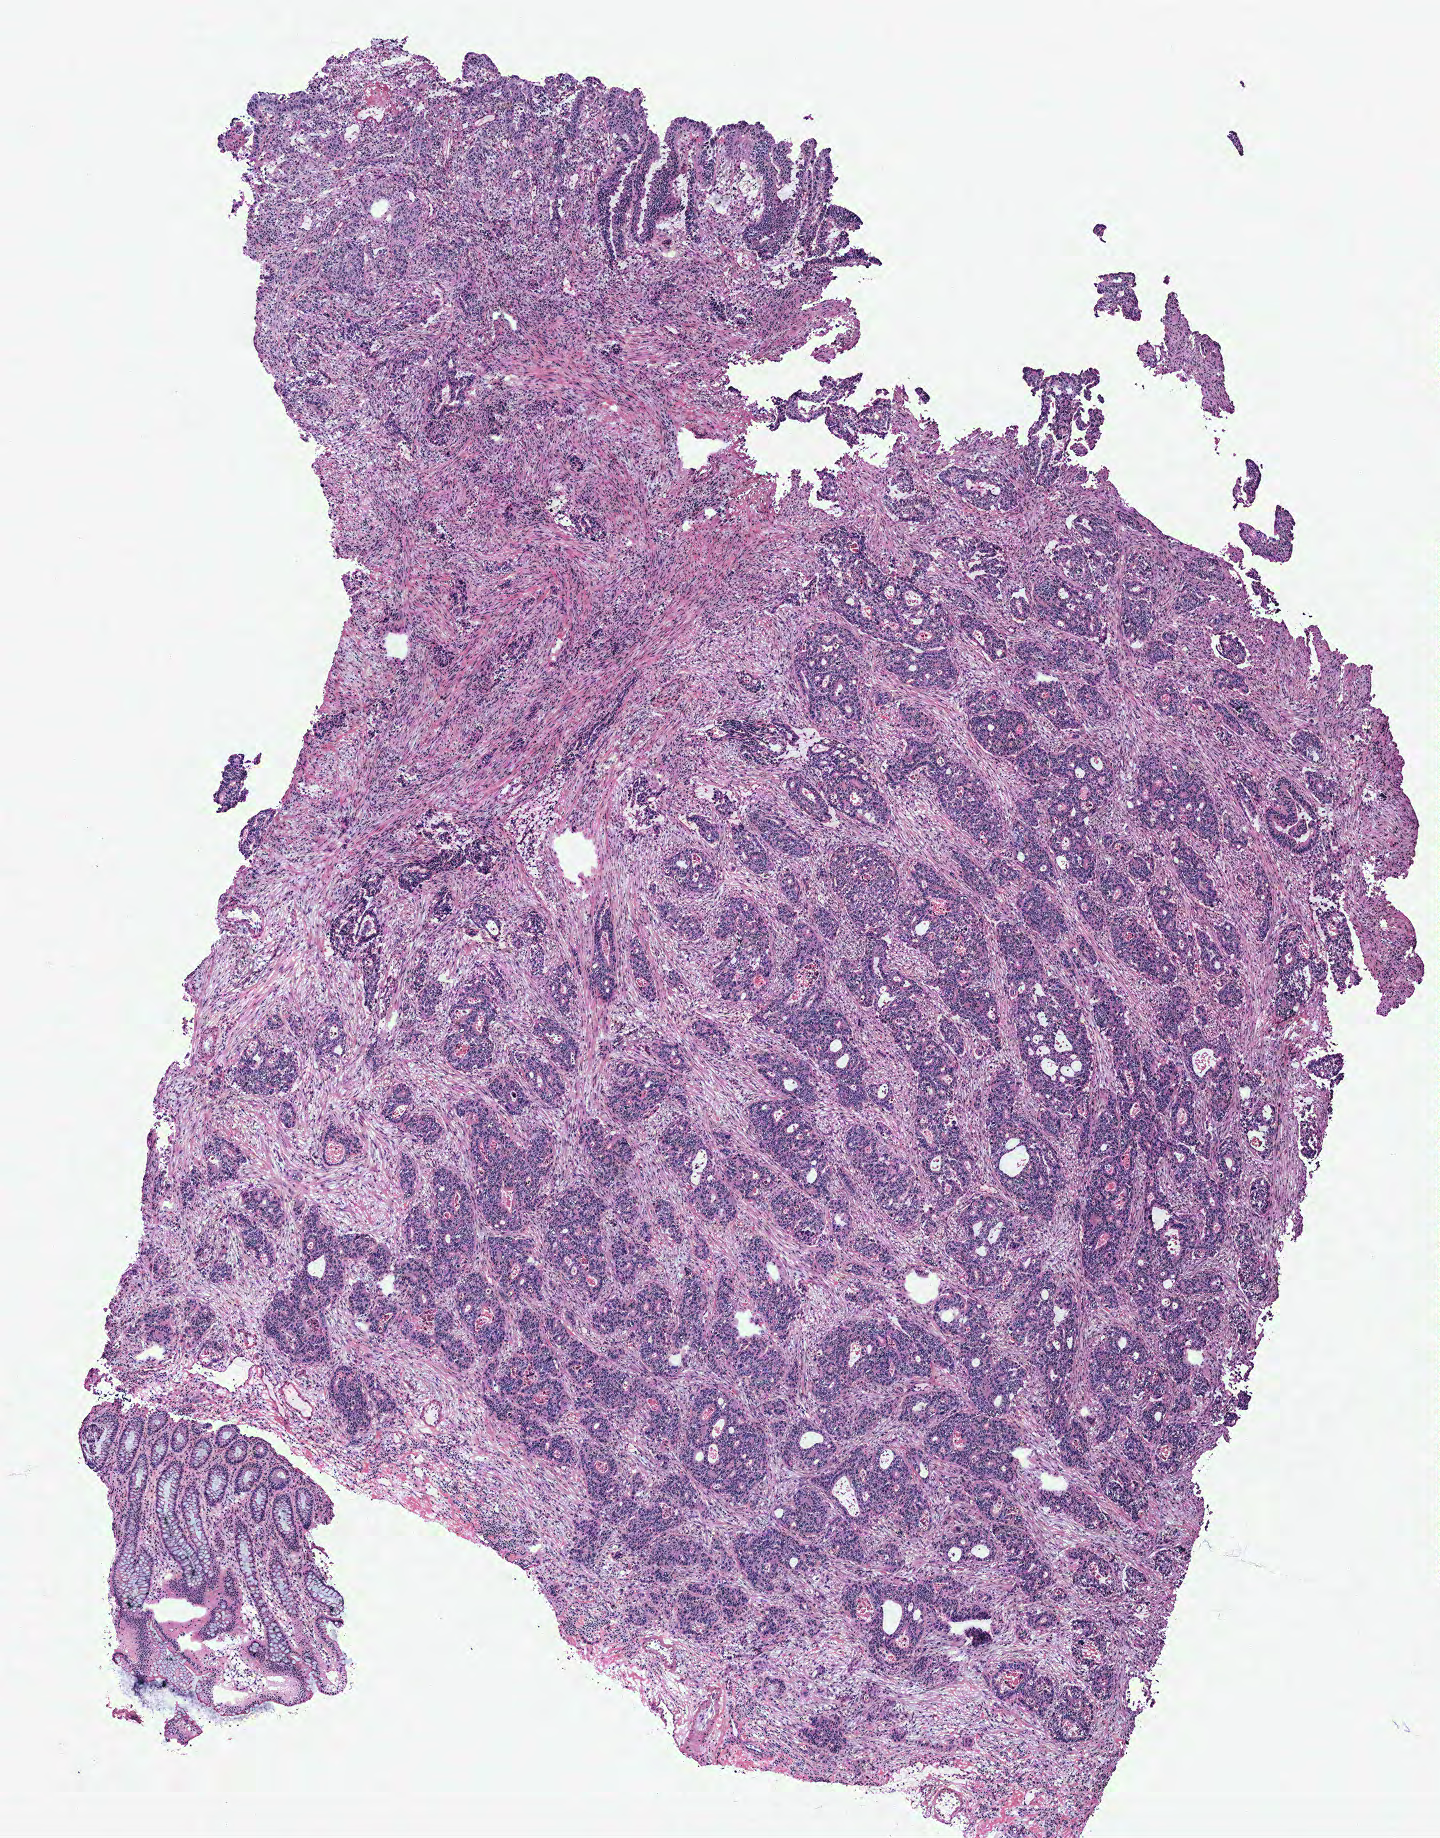
Whole-slide histology image, H&E — shown as a low-resolution overview of the whole scanned area (about 5.8 x 7.4 mm); colon, tissue type not recorded.
* patient diagnosis (cohort enrolment): colon cancer (colon)